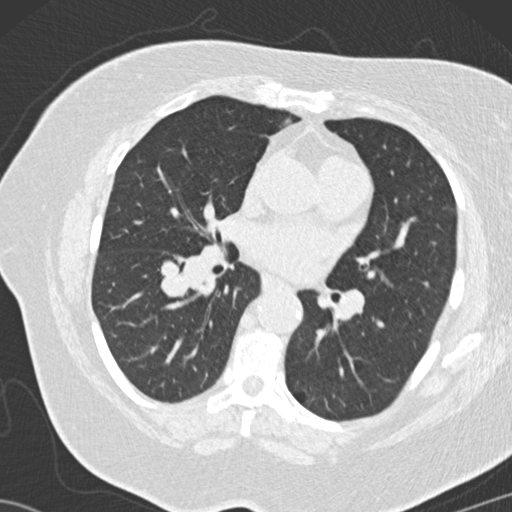
Low-dose screening chest CT, one axial slice. Position 71 of 146 along the scan axis. 120 kVp. Lung window (W 1500 / L -600 HU). 2 mm slice thickness. 512 × 512 image matrix, field of view 350 × 350 mm.
Annotated regions visible in this slice (expert manual segmentation):
- lesion 4 (tumor, lower lobe of right lung): bounding box (x1, y1, x2, y2) in pixels: (160, 260, 190, 298)